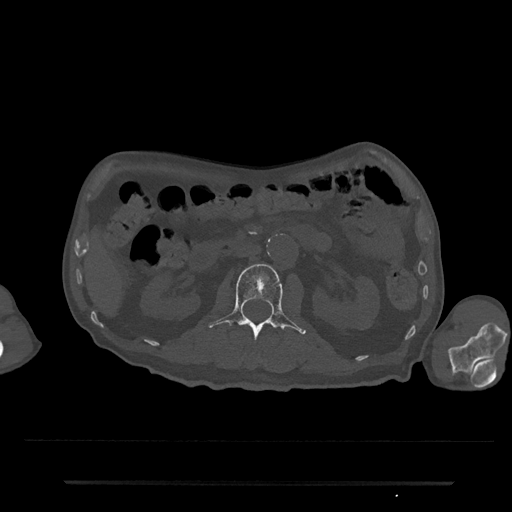
CT including the spine, one axial slice. Slice 69 of 797 in the series (ordered by position). 120 kVp. Bone window (W 1800 / L 400 HU). 512 × 512 image matrix, field of view 427 × 427 mm. Male patient, age 74 years. Case-level facts recorded for this patient, not image findings: primary cancer: prostate.
Annotated regions visible in this slice (semi-automatically segmented with operator editing):
- L2 vertebra: box from (x=208, y=263) to (x=306, y=338) px